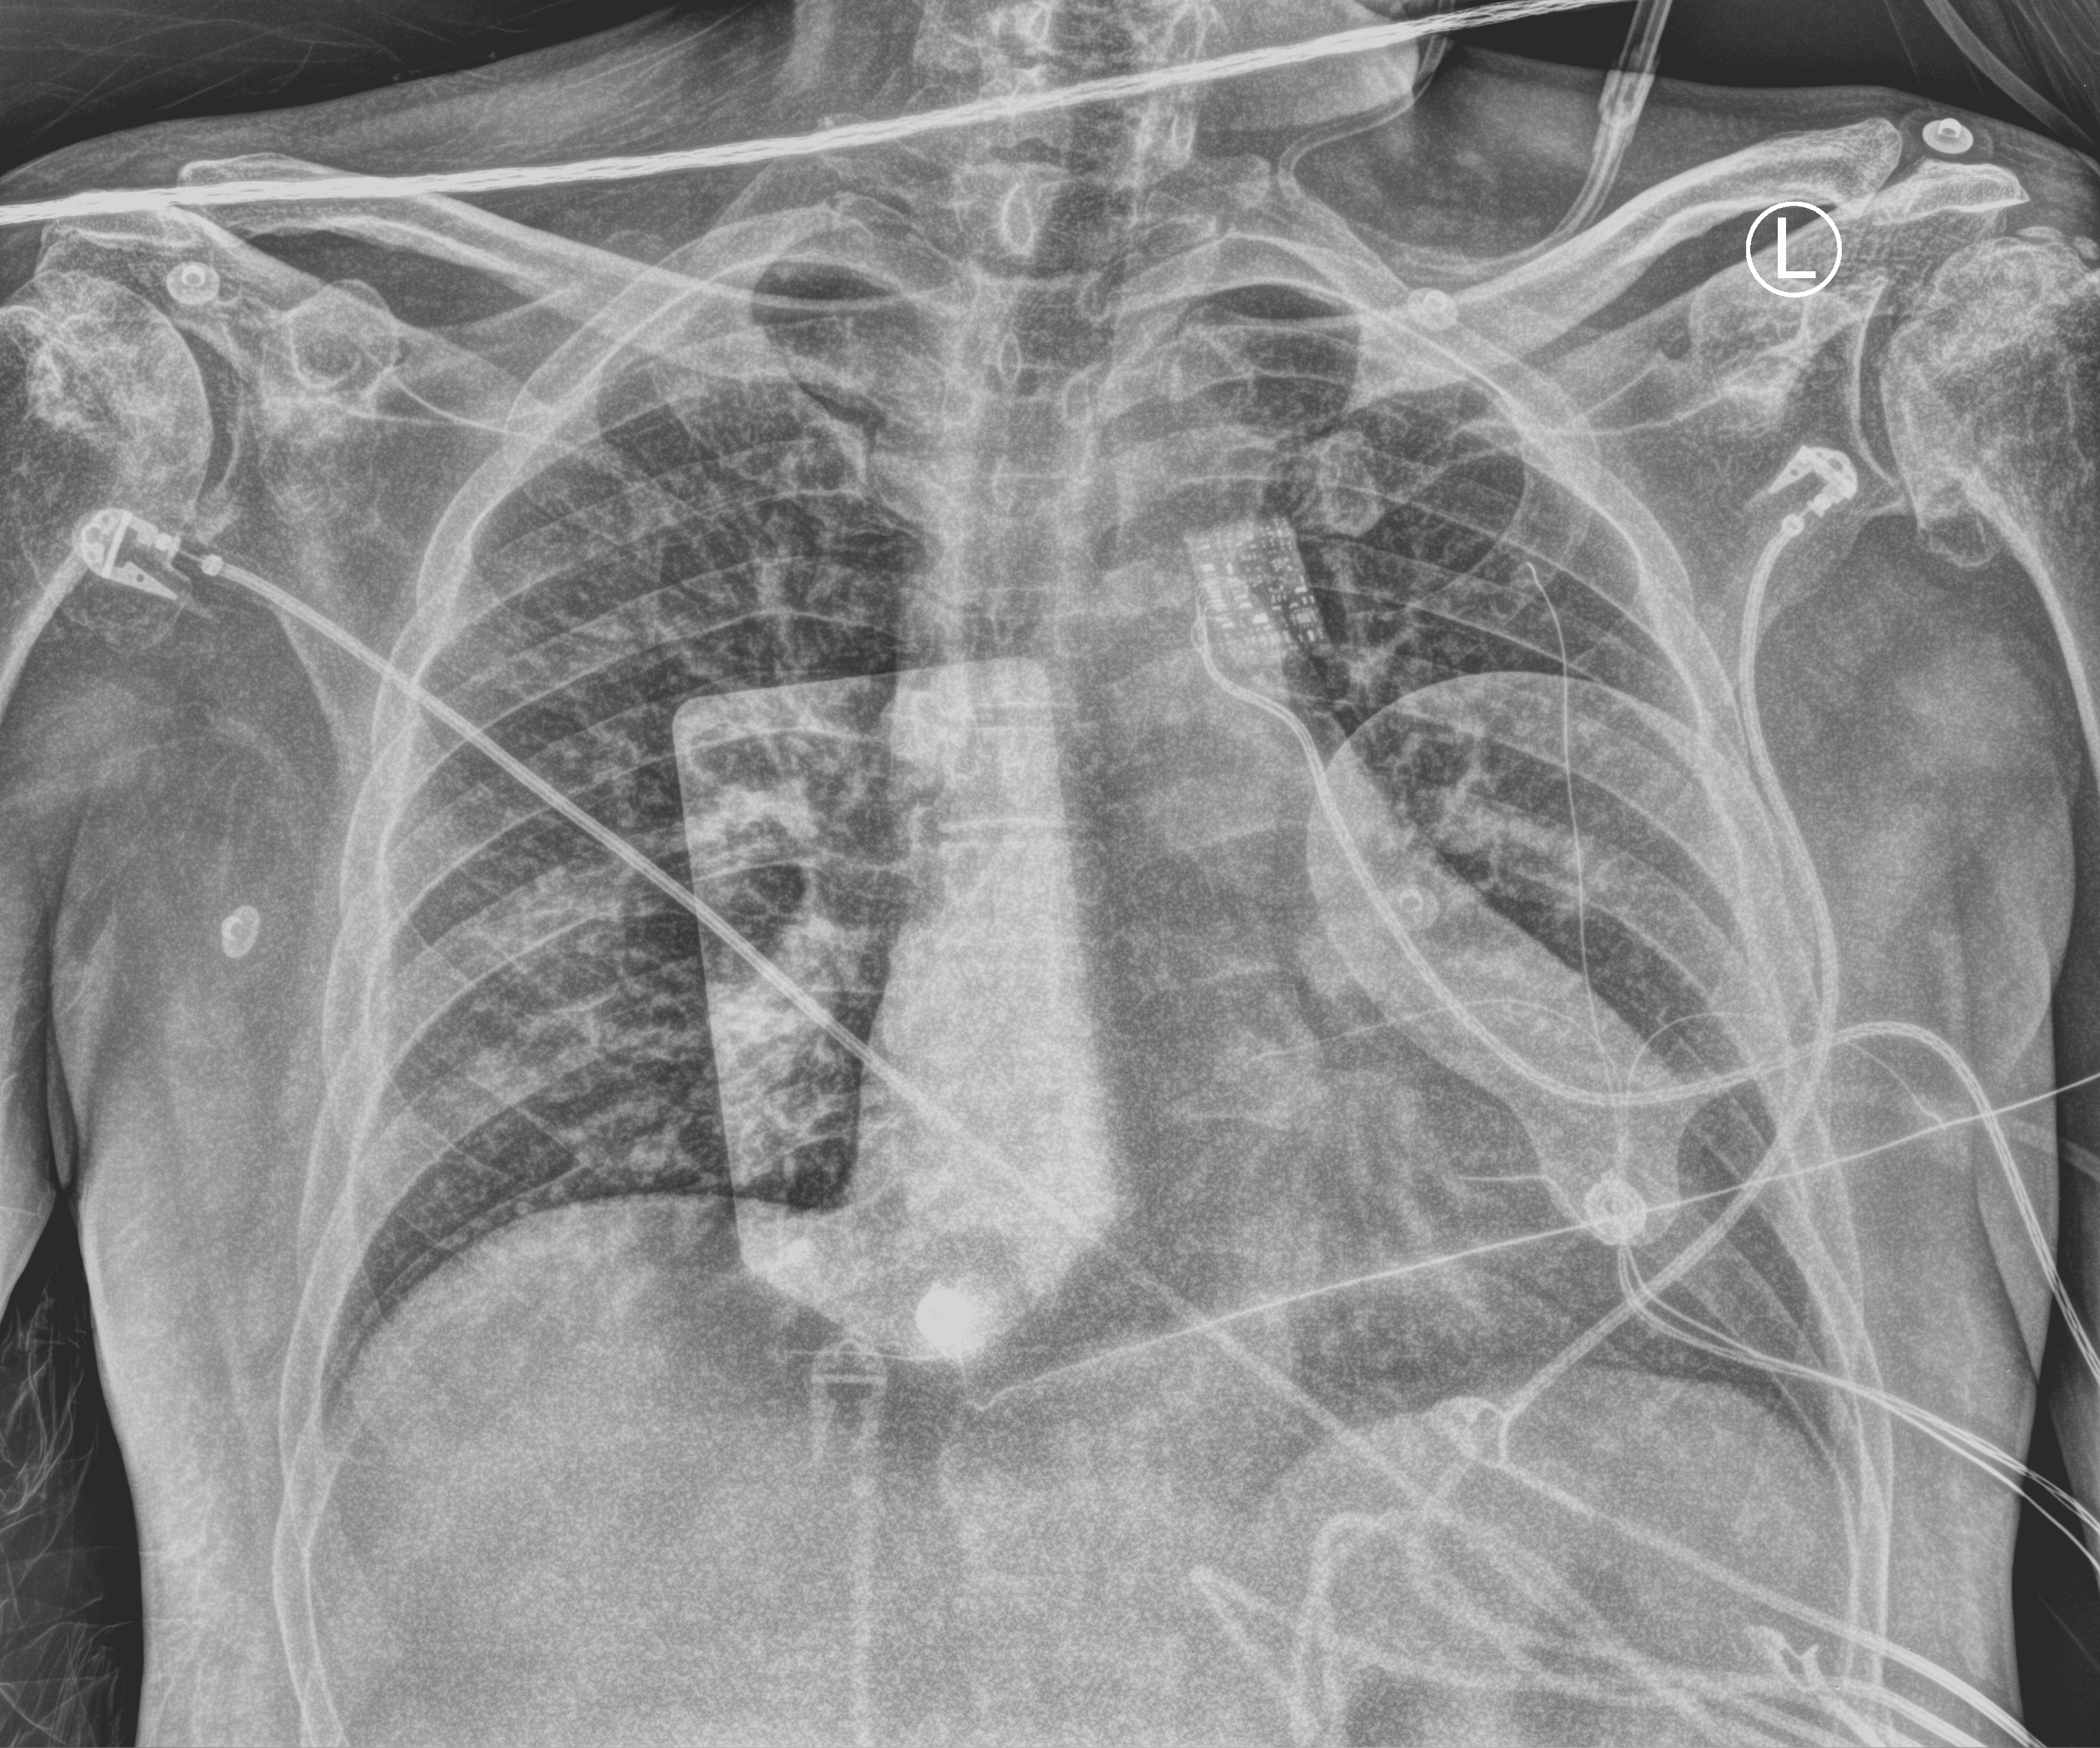
Chest X-ray (portable), anteroposterior (AP) projection. Patient hospitalised with COVID-19; male, aged 60–74 years.
Hospital-stay facts (about this admission, not read from this image; timing relative to this image not recorded):
- length of hospital stay: 3 days